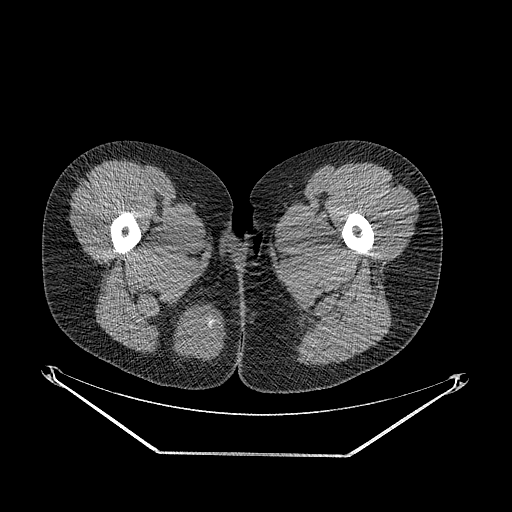
CT of an extremity soft-tissue mass (from a PET/CT study), one axial slice. Slice 24 of 267 in the series (ordered by position). Soft-tissue window (W 400 / L 40 HU). 3.75 mm slice thickness. 512 × 512 image matrix, field of view 500 × 500 mm. Female patient. From the clinical record (not read from this slice): histological type: epithelioid sarcoma; grade: intermediate; site of the primary tumour: right buttock.
Structures marked on this image (expert contour drawn on MRI and transferred to this co-registered scan by the dataset authors):
- gross tumour volume including surrounding oedema: bounding box (x1, y1, x2, y2) in pixels: (169, 301, 225, 366)
- gross tumour volume (mass): (174, 306, 225, 359)